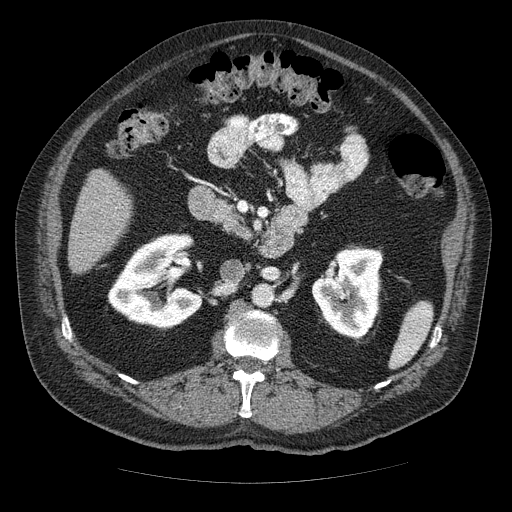
Contrast-enhanced abdominal CT (liver protocol), one axial slice. Slice 14 of 85 in the series (ordered by position). 120 kVp. Soft-tissue window (W 400 / L 40 HU). 2.5 mm slice thickness. 512 × 512 image matrix, field of view 420 × 420 mm. Case-level facts recorded for this patient, not image findings: diagnosis: hepatocellular carcinoma (patient treated with transarterial chemoembolisation; whether this scan precedes or follows treatment is not stated here); TNM stage (as recorded): Stage-IIIA; Child-Pugh class: A; tumour size: 7 cm.
Outlined on this slice (semi-automatically segmented with operator editing):
- liver parenchyma outside the tumour (the mass and vessels are separate outlines, so this box may not span the whole liver): box from (x=68, y=168) to (x=132, y=272) px